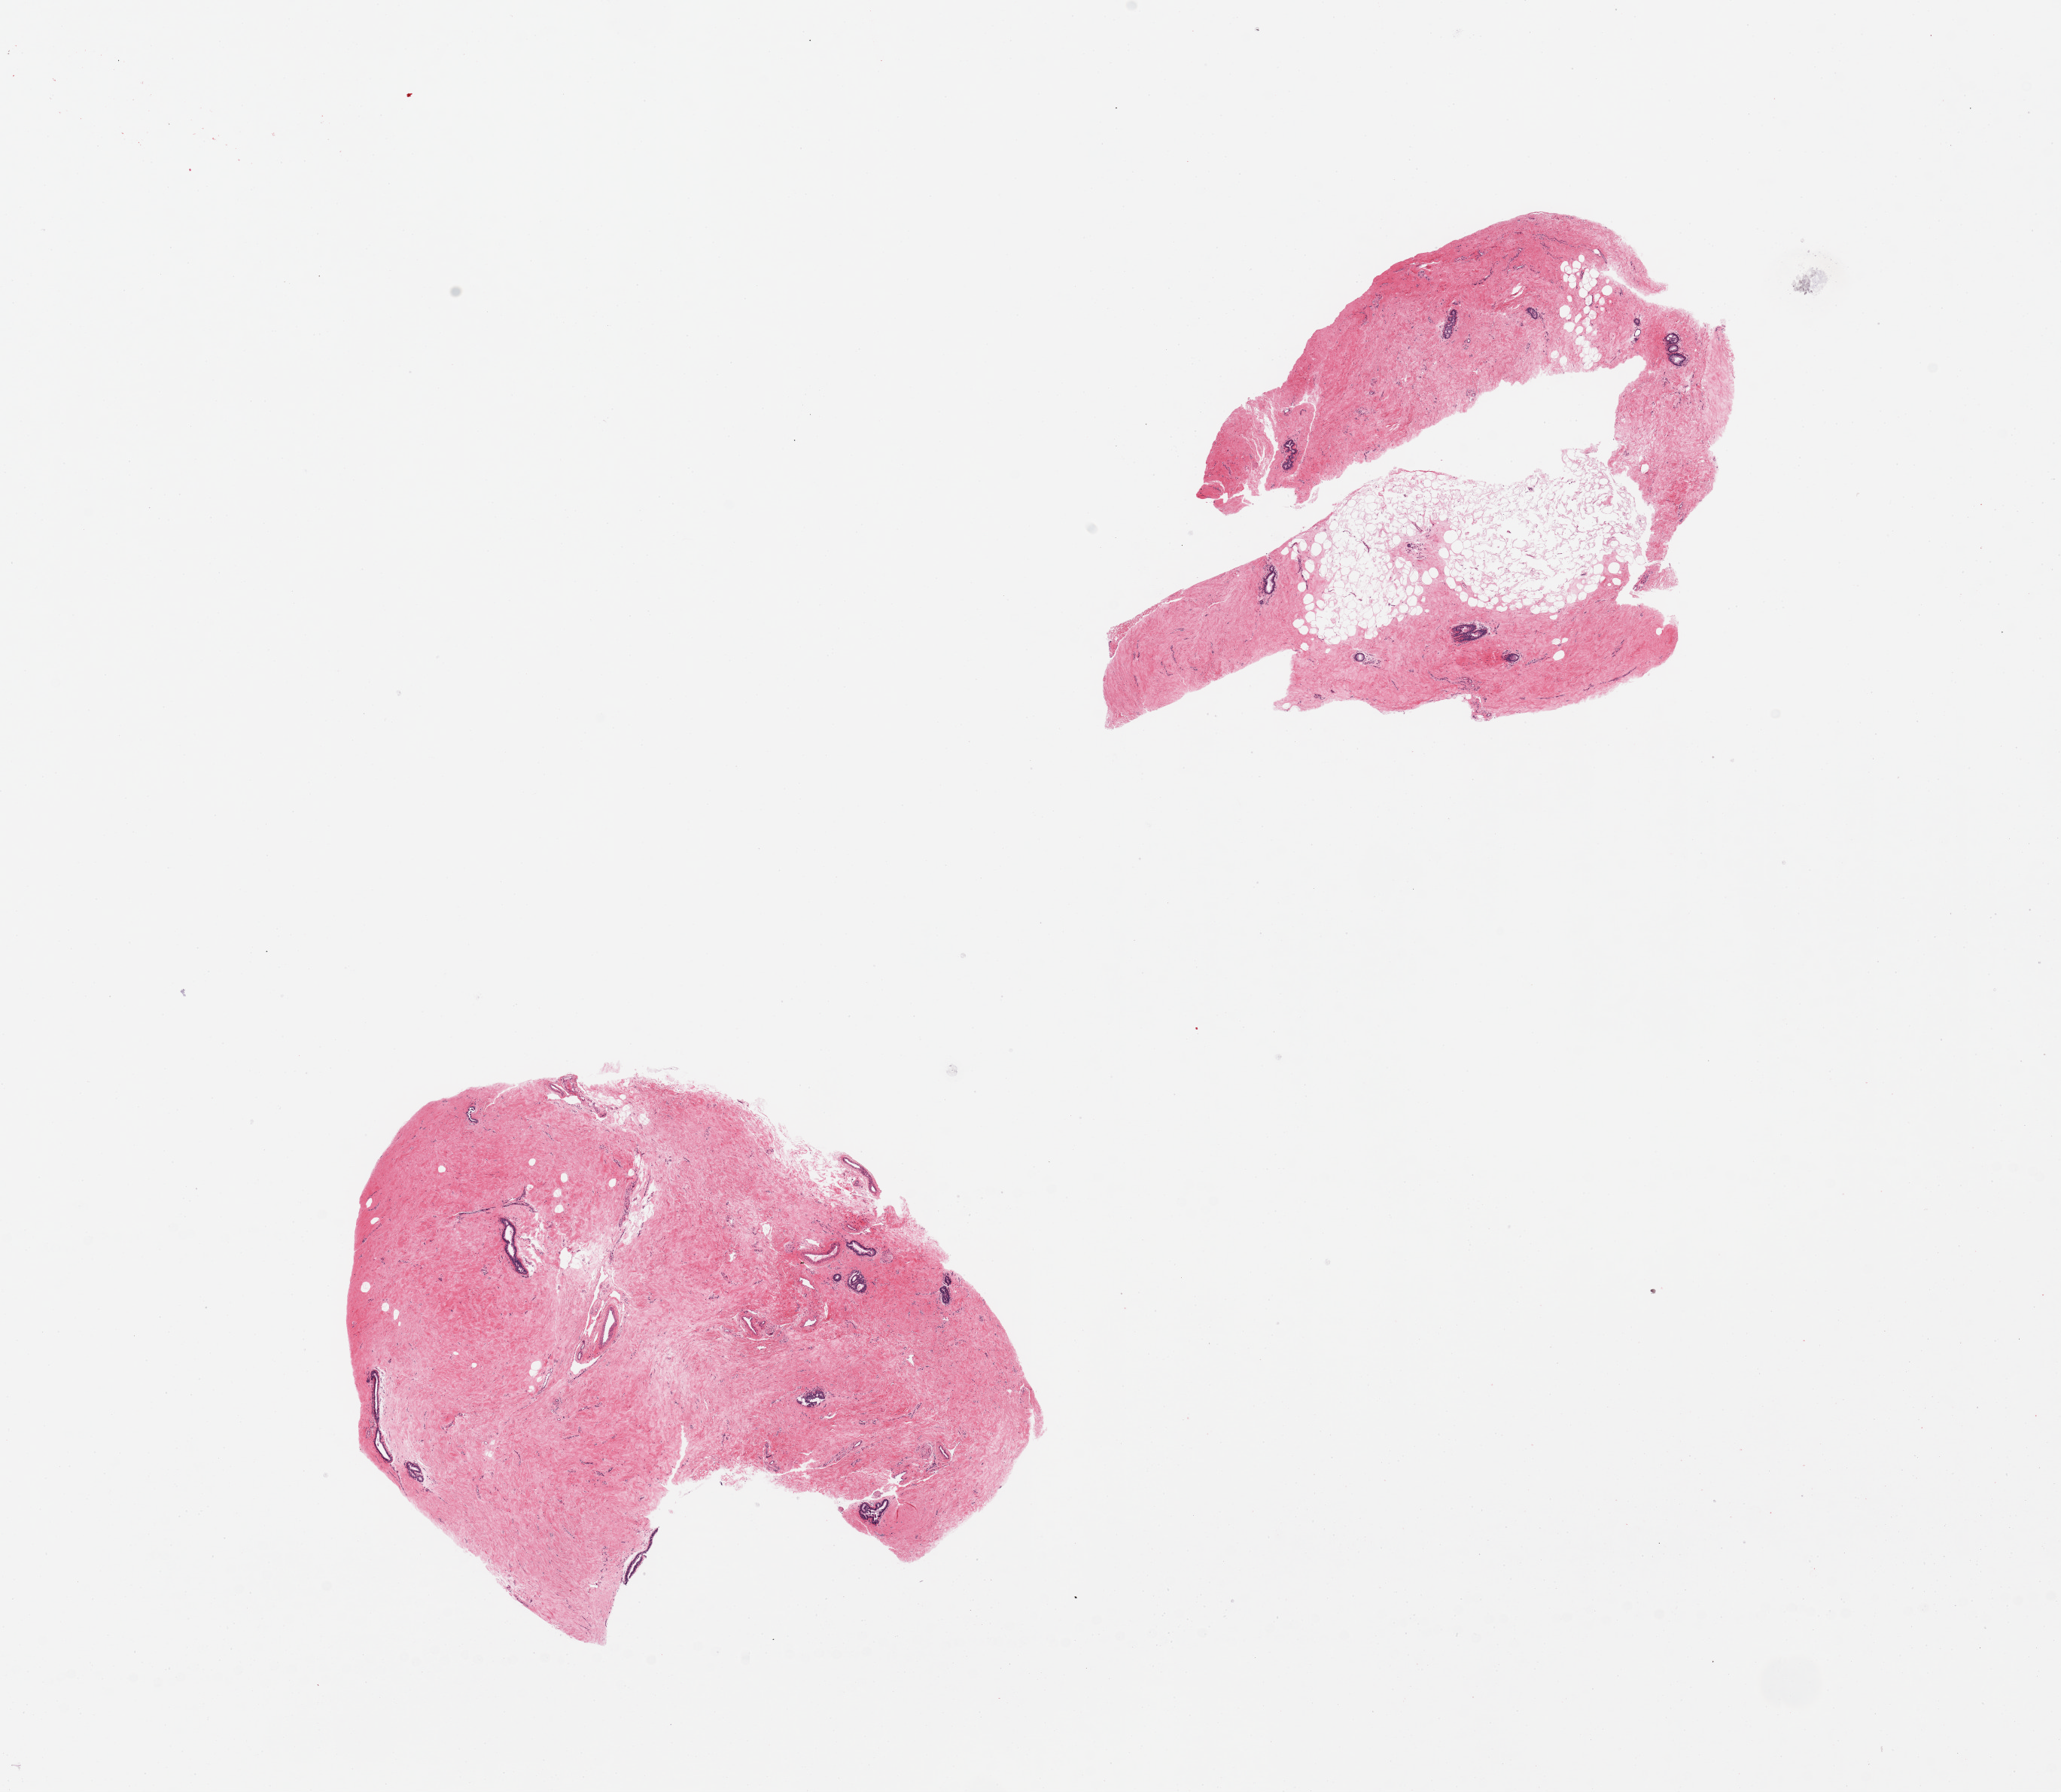
Whole-slide image, haematoxylin and eosin stain, shown as a low-resolution overview of the whole scanned area (about 21.7 x 18.8 mm); PAXgene-fixed, paraffin-embedded tissue; section of breast (target tissue); donor tissue sample. Male donor.
Reviewer comment on this tissue sample: 2 pieces. gynecomastia with stromal and ductal hyperplasia.